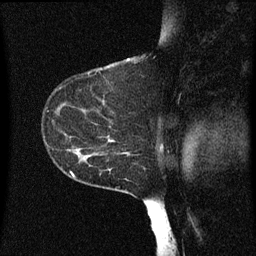
Breast MRI (dynamic contrast-enhanced), one sagittal slice. Dynamic contrast-enhanced series, image 2 of 3 at this slice position (ordered by acquisition). 1.5 T. TE 4.2 ms, TR 8 ms. 2 mm slice thickness. 256 × 256 image matrix, field of view 200 × 200 mm. Patient: female, 55 years.
Annotated regions visible in this slice (semi-automatic segmentation, software-assisted and operator-edited):
- analysis volume of interest (the breast-tissue region the enhancement analysis was run in; not a lesion): bounding box <46,124,151,183> (left, top, right, bottom; pixels)
- tumour enhancement mask (voxels above the 70 % enhancement threshold inside the analysis volume of interest): <100,136,127,157>